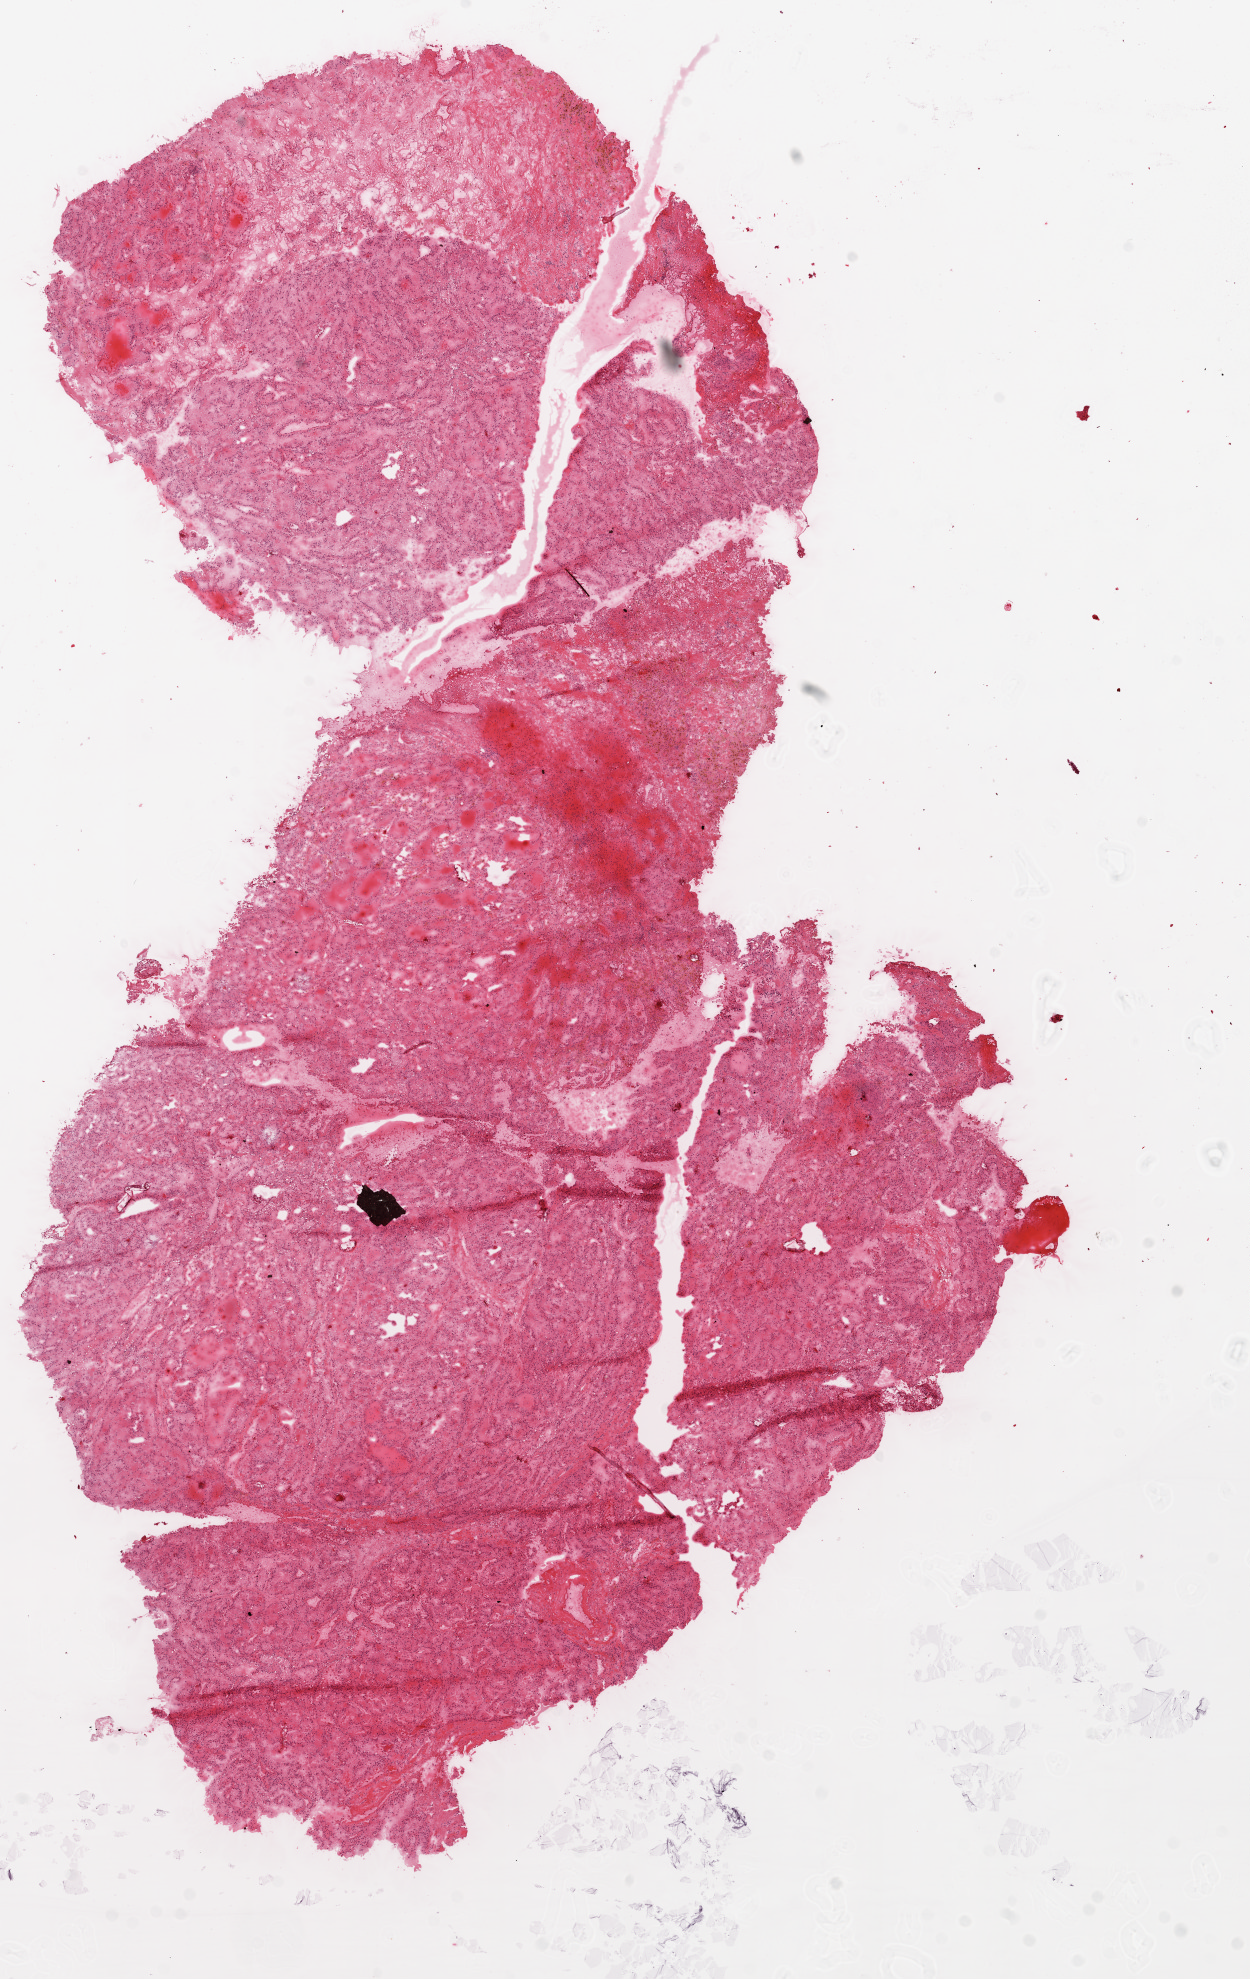
Digitized H&E-stained tissue section (whole slide) — shown as a low-resolution overview of the whole scanned area (about 10.0 x 15.9 mm, from a 20x scan). Frozen section from the top of the tissue portion. Primary tumour sample from the kidney. Male, age 49 years at initial diagnosis. Histologic grade: G3 (poorly differentiated). Slide review estimates, as recorded: tumour cells 90%, tumour nuclei 85%, normal cells 0%, stromal cells 10%, necrosis 0%.
Histologic diagnosis: Clear cell adenocarcinoma, NOS. AJCC pathologic stage: I.